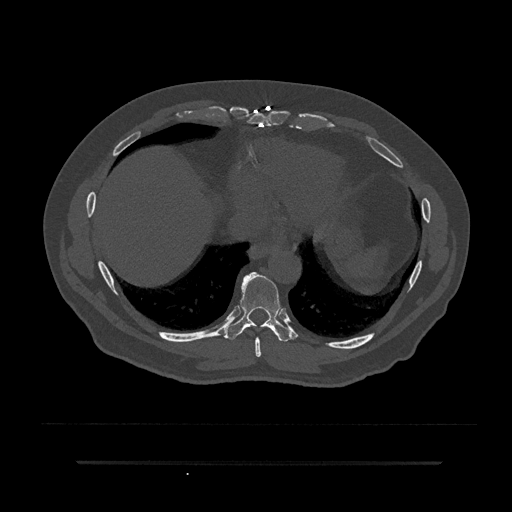
CT including the spine, one axial slice; slice 390 of 797 in the series (ordered by position); bone window (W 1800 / L 400 HU); 0.5 mm slice thickness; 512 × 512 image matrix. Male patient, age 59 years. From the clinical record (not read from this slice): primary cancer: bile ducts.
Outlined on this slice (semi-automatic segmentation, software-assisted and operator-edited):
- T8 vertebra: bounding box <255,337,261,357> (left, top, right, bottom; pixels)
- T9 vertebra: <226,272,291,342>